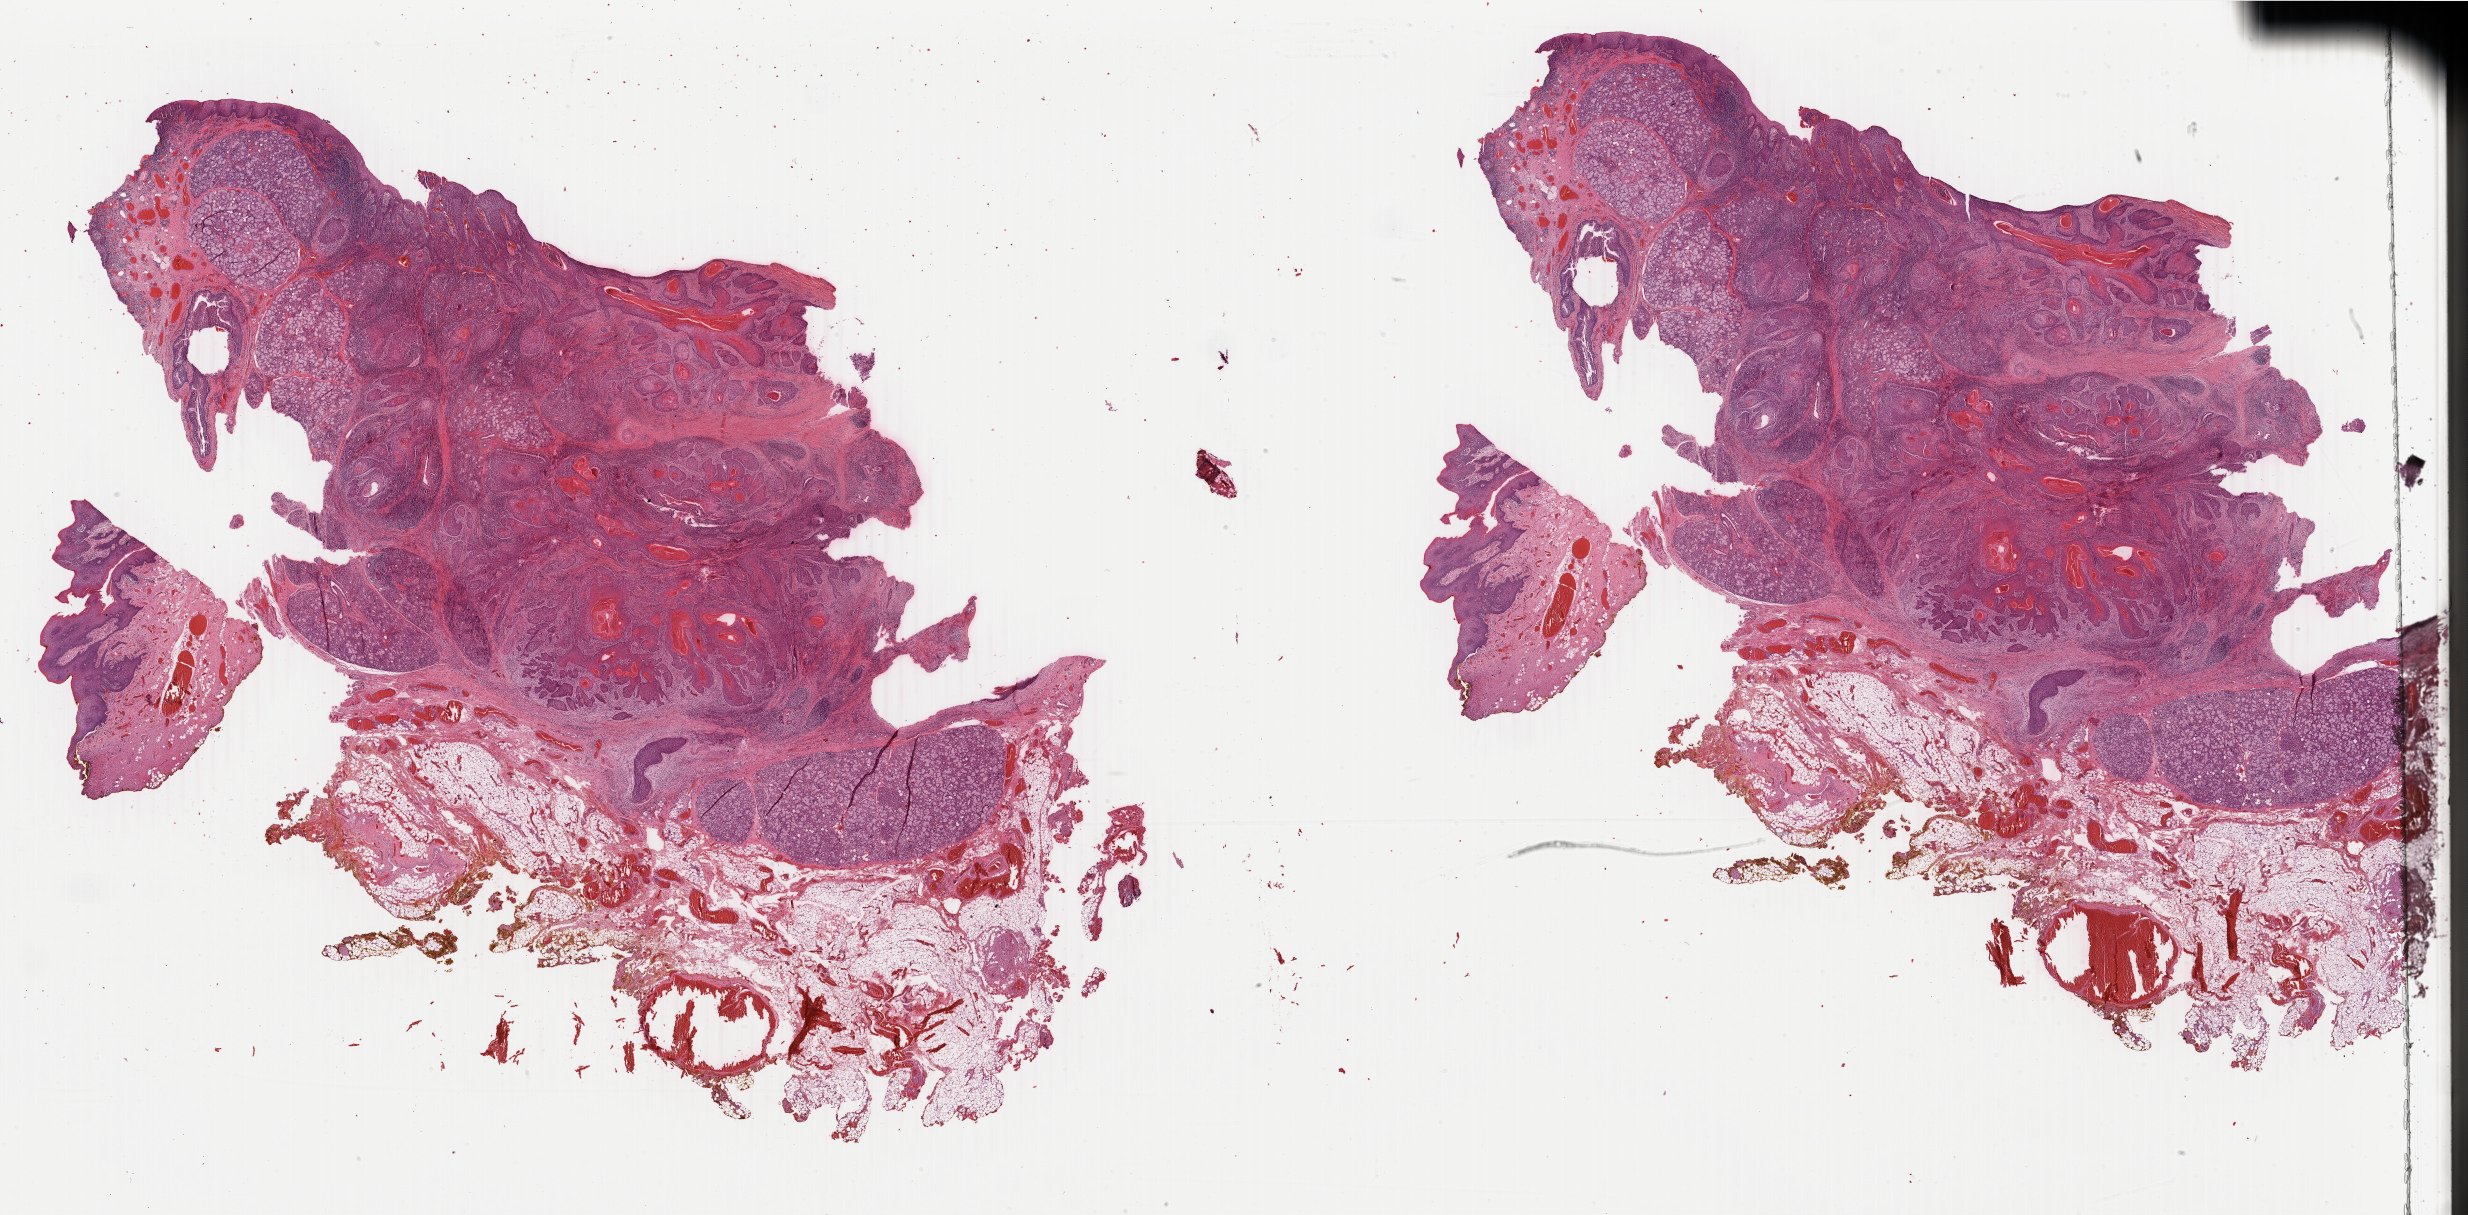
Digitized H&E tissue section (whole slide), low-resolution overview of the scanned area, about 39.3 x 19.3 mm (acquisition: 40x scan), formalin-fixed paraffin-embedded (FFPE) diagnostic section, sample: primary tumour, head and neck. Male patient; age at initial diagnosis 57 years. Histologic grade: G2 (moderately differentiated).
- pathologic diagnosis: Squamous cell carcinoma, keratinizing, NOS (floor of mouth, NOS)
- TNM: T4a N2c MX
- laterality: midline
- AJCC pathologic stage: IVA (7th edition)